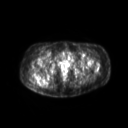
FDG PET of an extremity soft-tissue mass (from a PET/CT study), one axial slice. Position 46 of 267 along the scan axis. 128 × 128 image matrix, field of view 600 × 600 mm. Female patient, age 60 years. Case-level facts recorded for this patient, not image findings: histological type: spindle cell suggestive of myxofibrosarcoma; grade: intermediate; site of the primary tumour: right buttock.
Outlined on this slice (expert contour drawn on MRI and transferred to this co-registered scan by the dataset authors):
- gross tumour volume (mass): box from (x=33, y=73) to (x=47, y=84) px